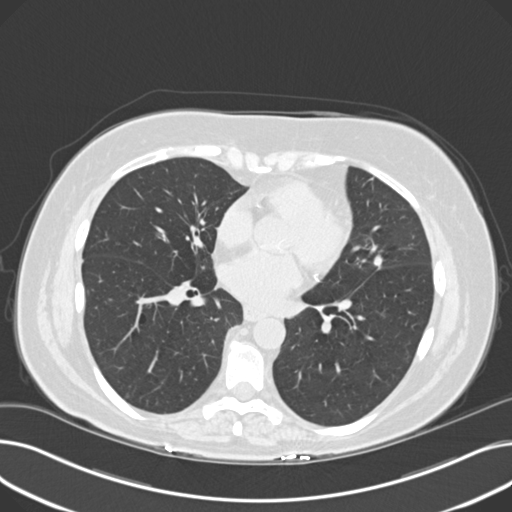
Low-dose screening chest CT, one axial slice; slice 90 of 203 in the series (ordered by position); reconstruction kernel B30f; 120 kVp; lung window (W 1500 / L -600 HU); 2 mm slice thickness; 512 × 512 image matrix, field of view 372 × 372 mm.
Structures marked on this image (outlined manually by an expert reader):
- lesion 1 (tumor, upper lobe of left lung): bounding box <373,255,384,269> (left, top, right, bottom; pixels)